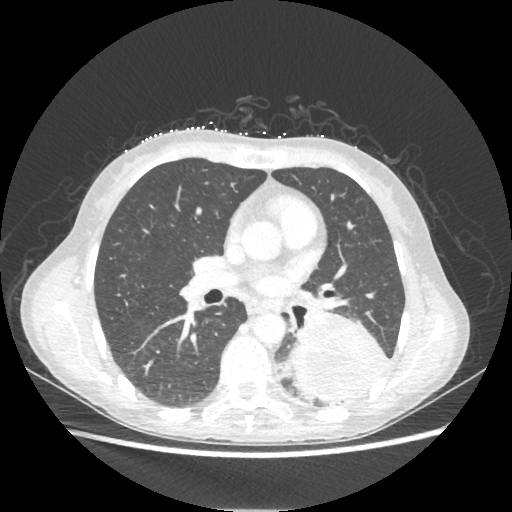
Chest CT, one axial slice. Slice 119 of 221 in the series (ordered by position). 80 kVp. Lung window (W 1500 / L -600 HU). 1.25 mm slice thickness. 512 × 512 image matrix, field of view 360 × 360 mm. Patient: female, 53 years. From the clinical record (not read from this slice): clinical TNM (as recorded): T3 N0 M0.
Structures marked on this image (bounding box drawn by a radiologist):
- lung tumour (recorded histology: adenocarcinoma): bounding box [x1, y1, x2, y2] px = [286, 309, 392, 406]